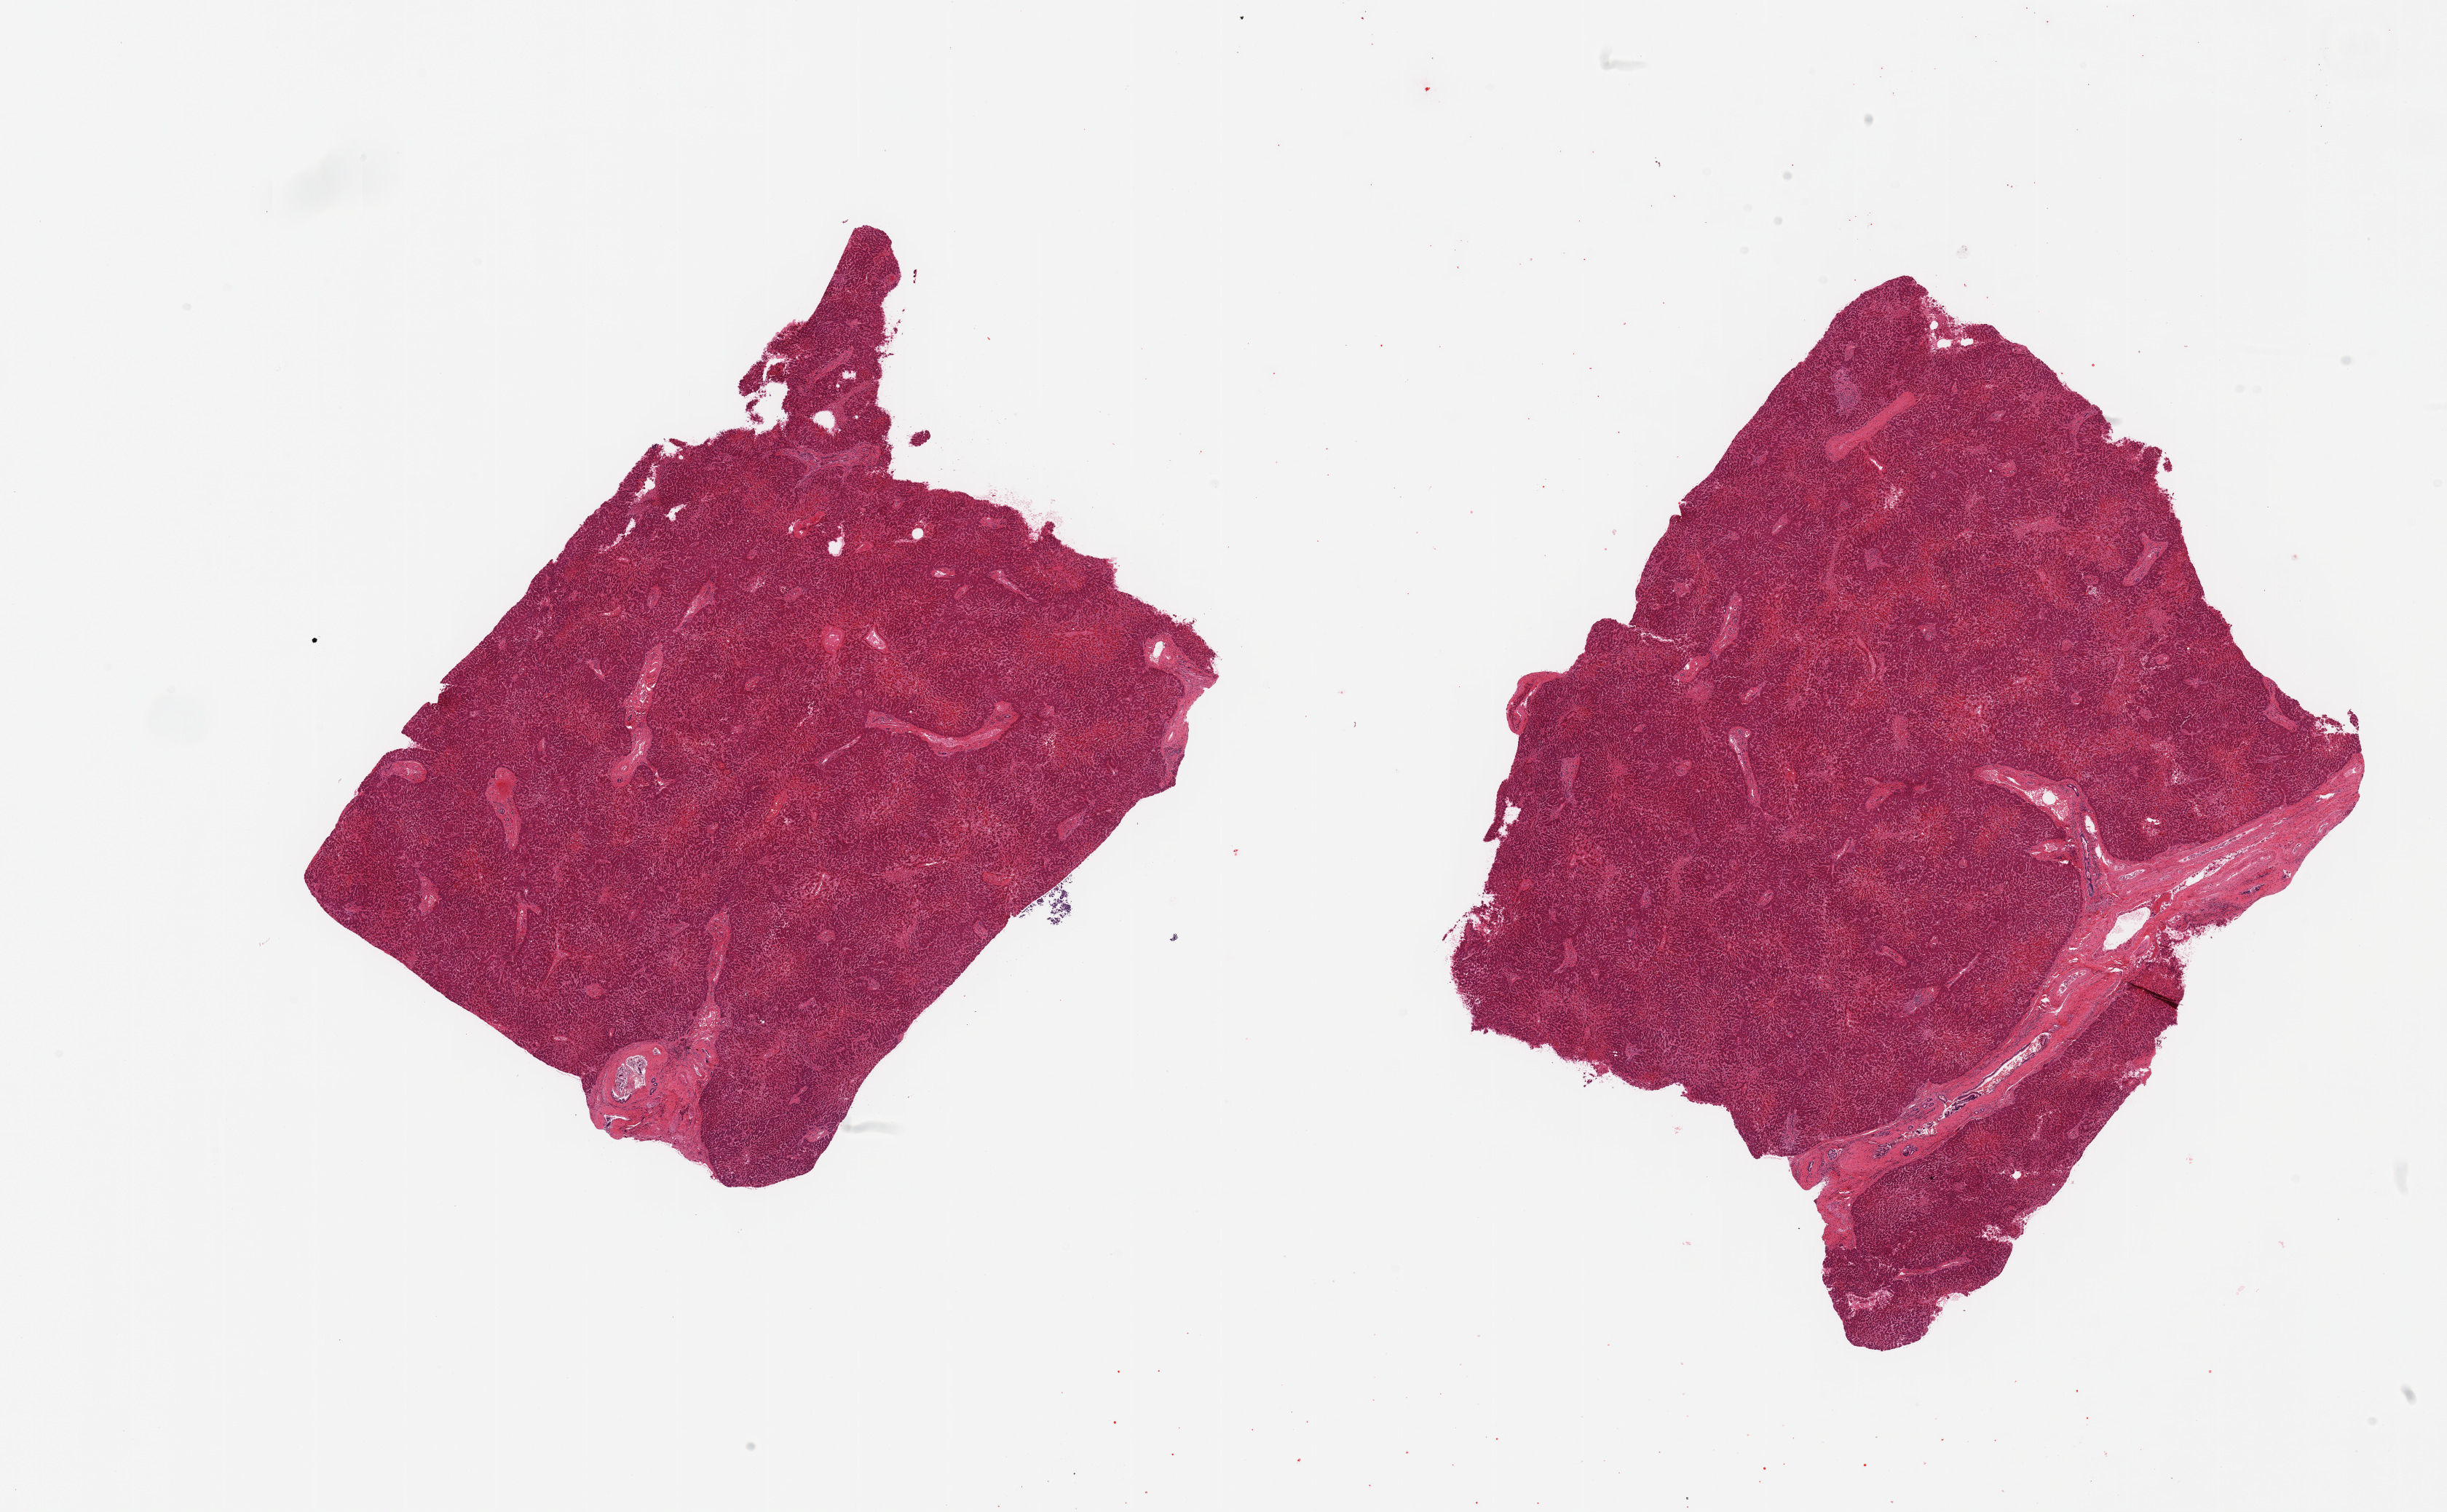
Hematoxylin and eosin (H&E) whole-slide image, a low-resolution overview of the entire scanned area, about 26.6 x 16.4 mm (from a 20x scan), PAXgene-fixed, paraffin-embedded tissue, sampled site (target tissue): liver, donor tissue sample. Male donor.
Reviewer comment on this tissue sample: 2 pieces, moderate passive congestion.